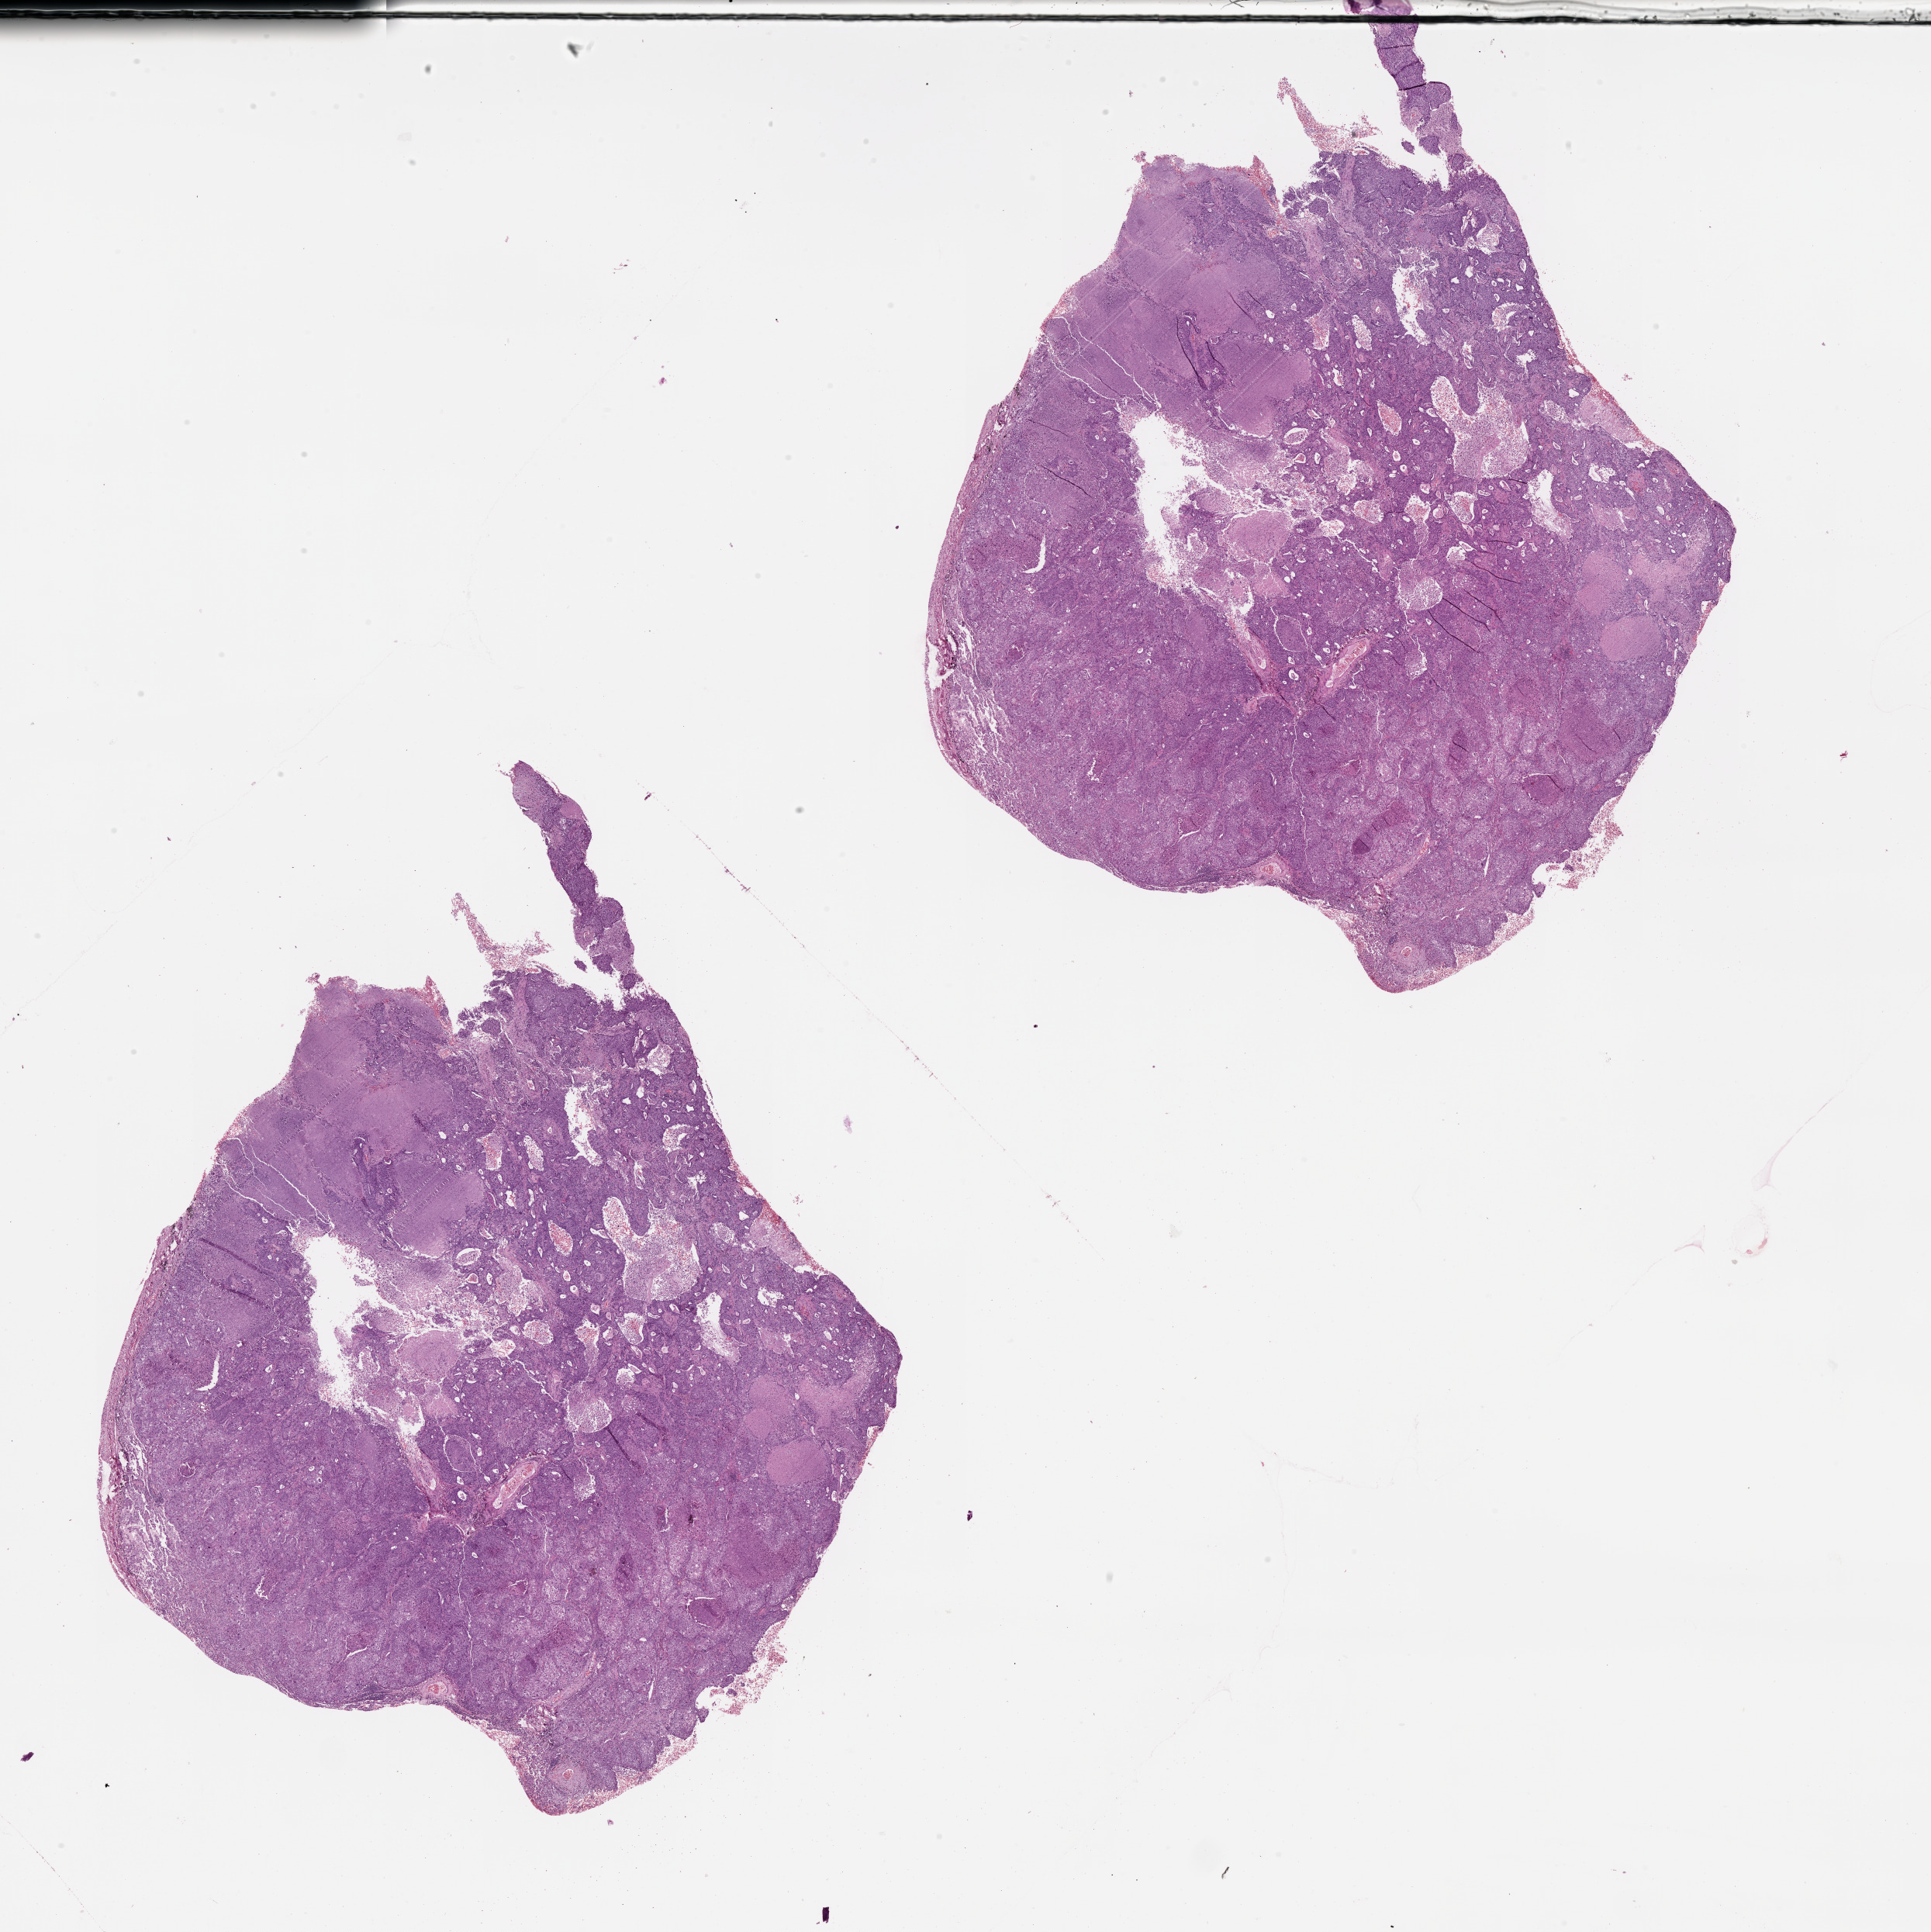
Whole-slide histology image, H&E, shown as a low-resolution overview of the whole scanned area (about 20.0 x 20.1 mm); lung, tumour tissue. Patient: male, age 63 years.
Patient diagnosis (cohort enrolment): squamous cell carcinoma (lung).